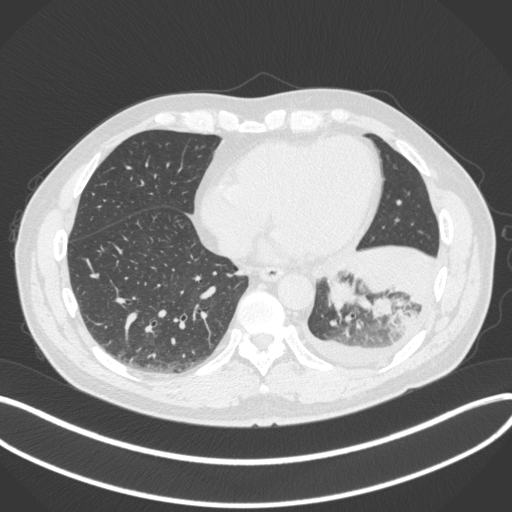
Chest CT, one axial slice. Position 111 of 350 along the scan axis. 120 kVp. Lung window (W 1500 / L -600 HU). 1 mm slice thickness. 512 × 512 image matrix, field of view 400 × 400 mm. Patient: male, 58 years. From the clinical record (not read from this slice): clinical TNM (as recorded): T3 N1 M1b; histopathological grade: G3.
Structures marked on this image (rectangle marked by the reading radiologist):
- lung tumour (recorded histology: small cell carcinoma): bounding box (x1, y1, x2, y2) in pixels: (324, 271, 366, 315)